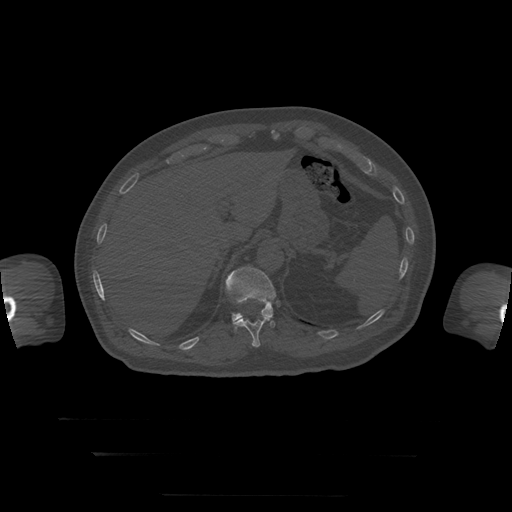
CT including the spine, one axial slice. Slice 88 of 397 in the series (ordered by position). Reconstruction kernel STANDARD. 120 kVp. Bone window (W 1800 / L 400 HU). 1.25 mm slice thickness. 512 × 512 image matrix, field of view 510 × 510 mm. Patient age 73 years. Case-level facts recorded for this patient, not image findings: primary cancer: prostate.
Annotated regions visible in this slice (semi-automatically segmented with operator editing):
- T11 vertebra: bounding box <233,313,276,348> (left, top, right, bottom; pixels)
- T12 vertebra: <226,267,276,330>